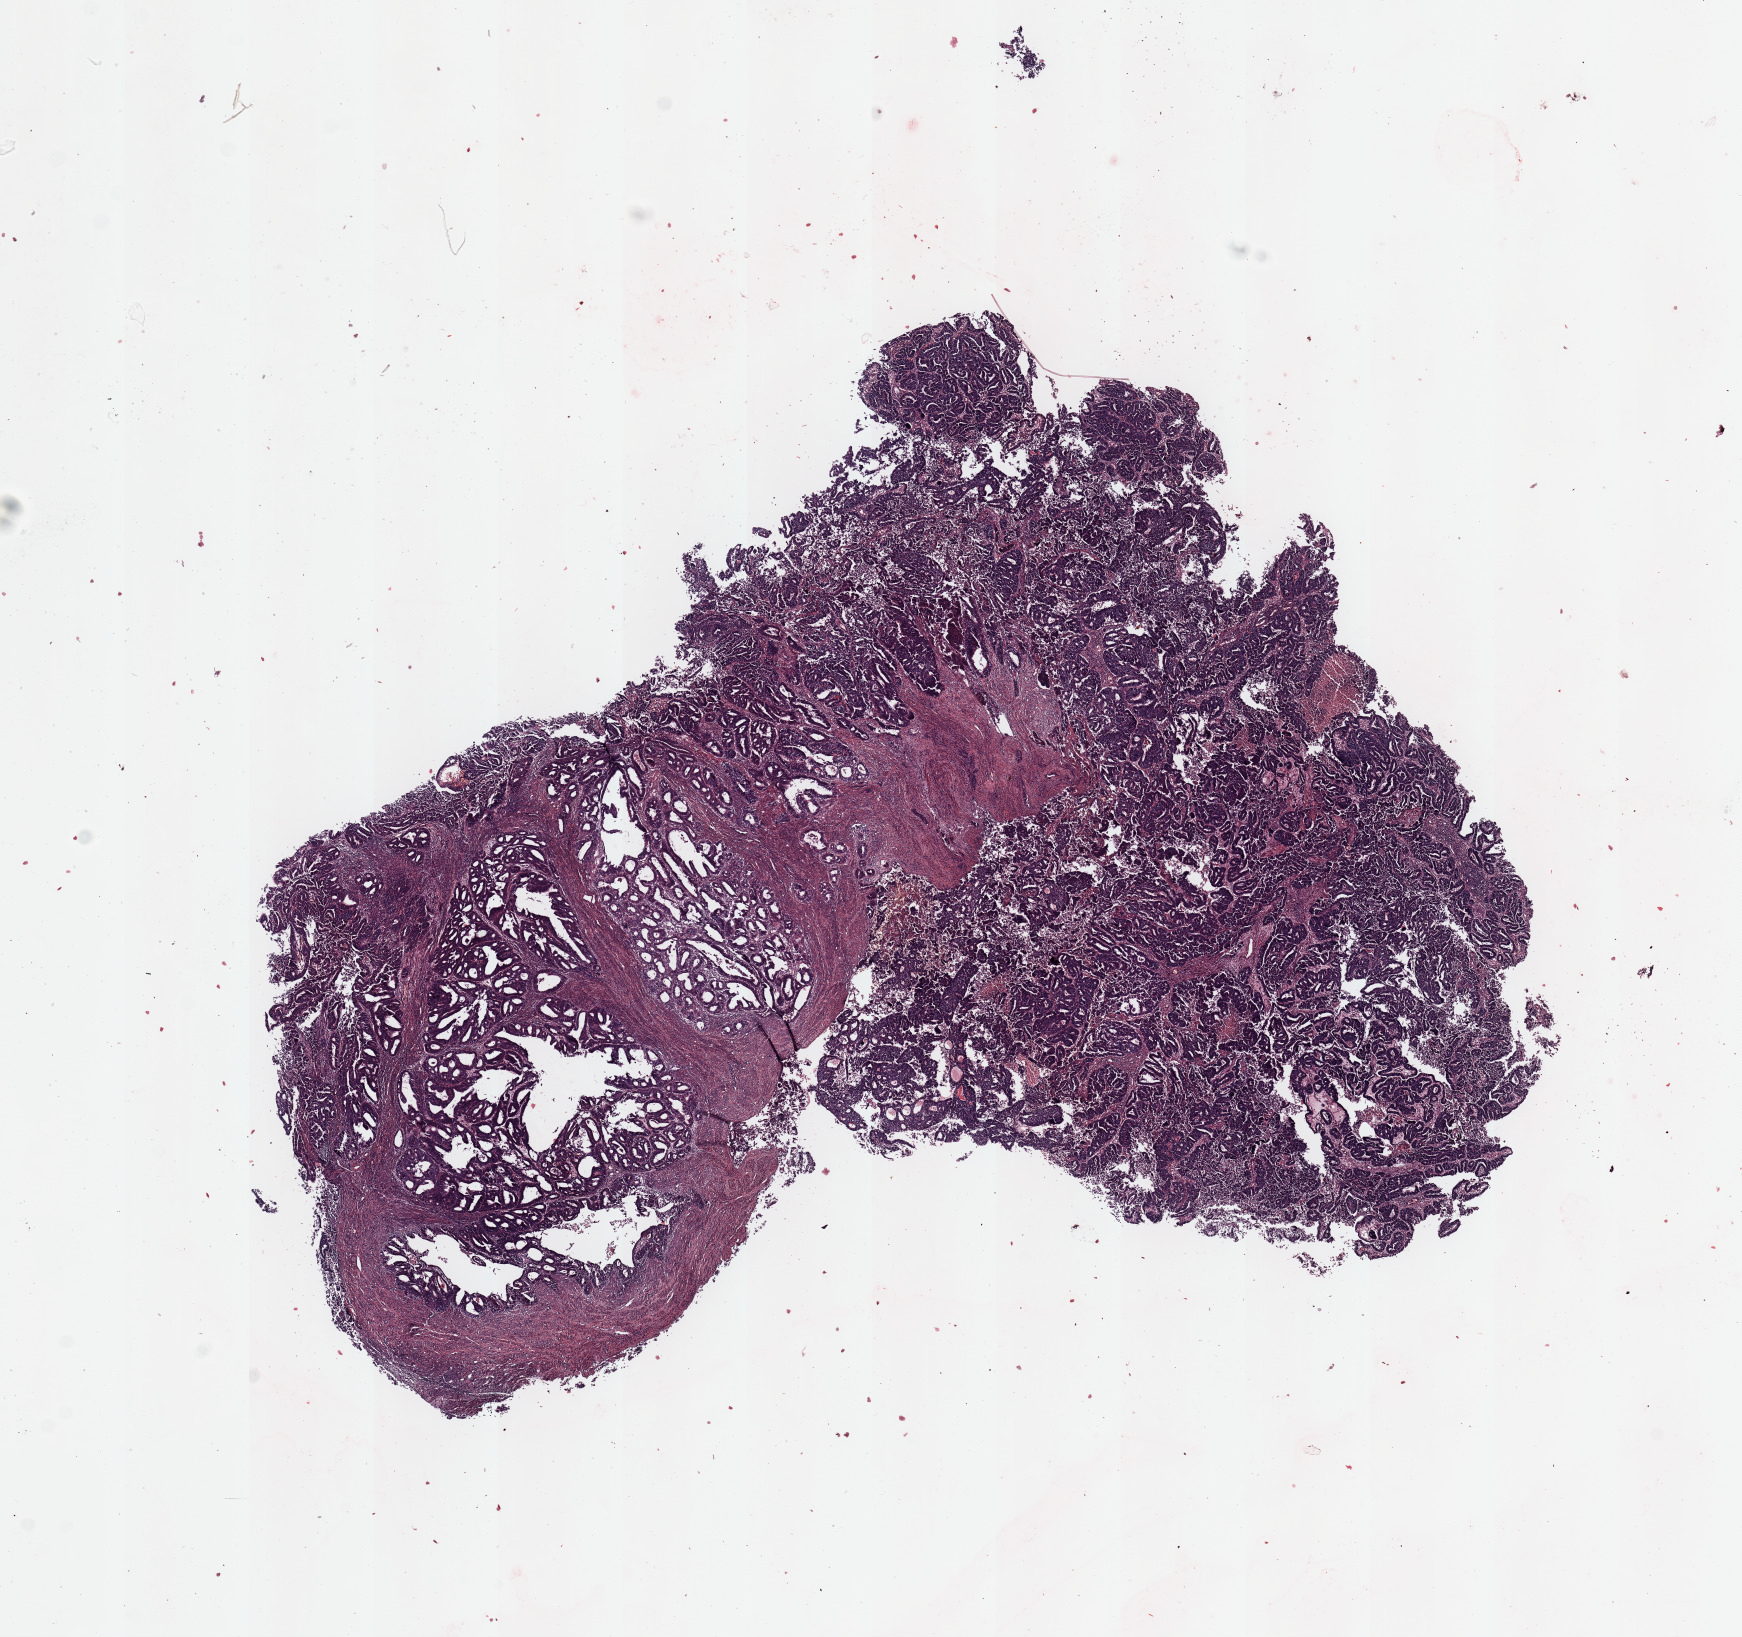
Digitized Hematoxylin and eosin (H&E) stained tissue section (whole slide), whole scanned area (about 13.8 x 13.0 mm) shown as a low-resolution overview, uterus, tumour tissue. Female, 67 y/o. Histologic grade: G2 (moderately differentiated).
AJCC pathologic stage: I. Diagnosis: Endometrioid adenocarcinoma, NOS.